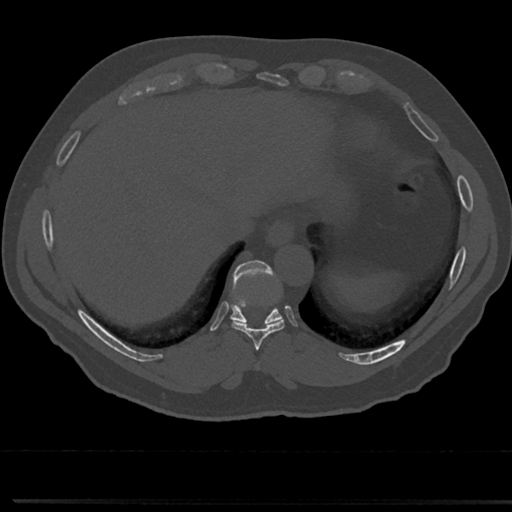
CT including the spine, one axial slice; slice 287 of 817 in the series (ordered by position); reconstruction kernel Br40s/3; 120 kVp; bone window (W 1800 / L 400 HU); 0.5 mm slice thickness; 512 × 512 image matrix. Patient: male, 61 years. From the clinical record (not read from this slice): primary cancer: prostate.
Structures marked on this image (semi-automatic segmentation, software-assisted and operator-edited):
- T8 vertebra: bounding box [x1, y1, x2, y2] px = [255, 344, 263, 372]
- T9 vertebra: [211, 264, 303, 350]